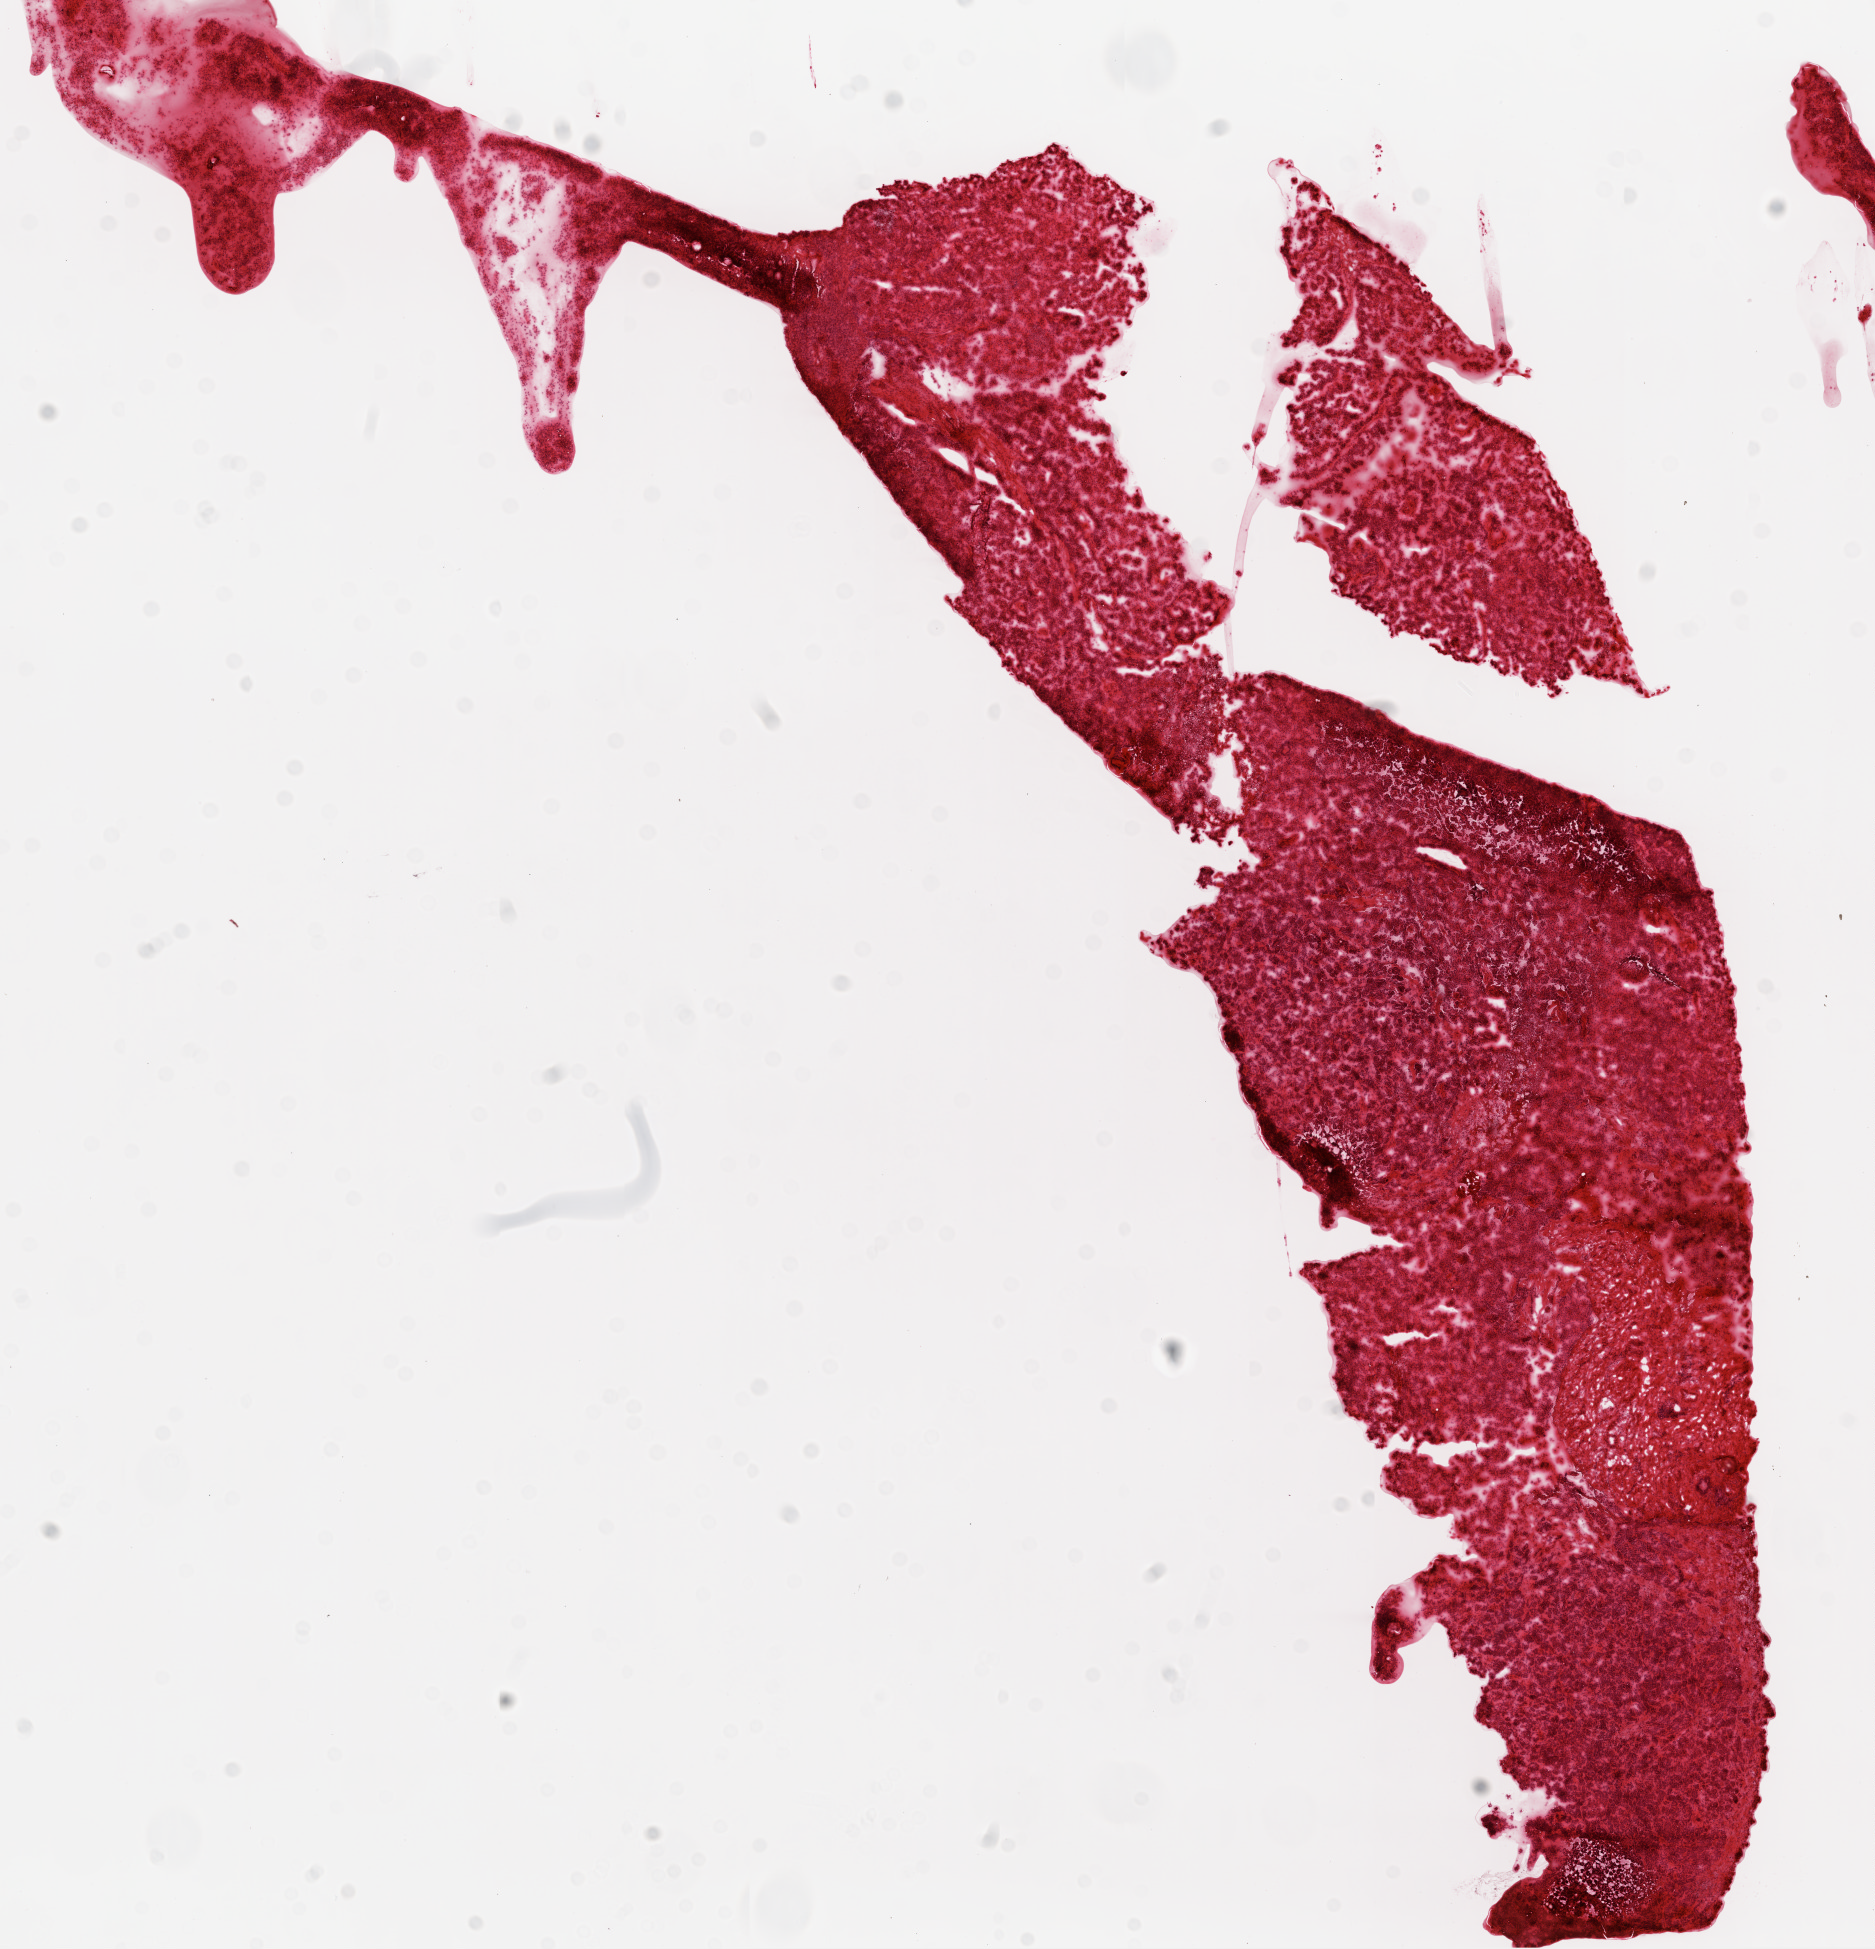
Hematoxylin and eosin (H&E) stained whole-slide image, low-resolution overview of the scanned area, about 15.0 x 15.6 mm (acquisition: 20x scan). Frozen section from the top of the tissue portion. Sample: primary tumour, ovary. Female patient; age at initial diagnosis 74 years. Histologic grade: G3 (poorly differentiated). Slide review estimates, as recorded: tumour cells 90%, tumour nuclei 90%, normal cells 0%, stromal cells 9%, necrosis 1%.
FIGO stage: IIIC. Diagnosis: Serous cystadenocarcinoma, NOS.